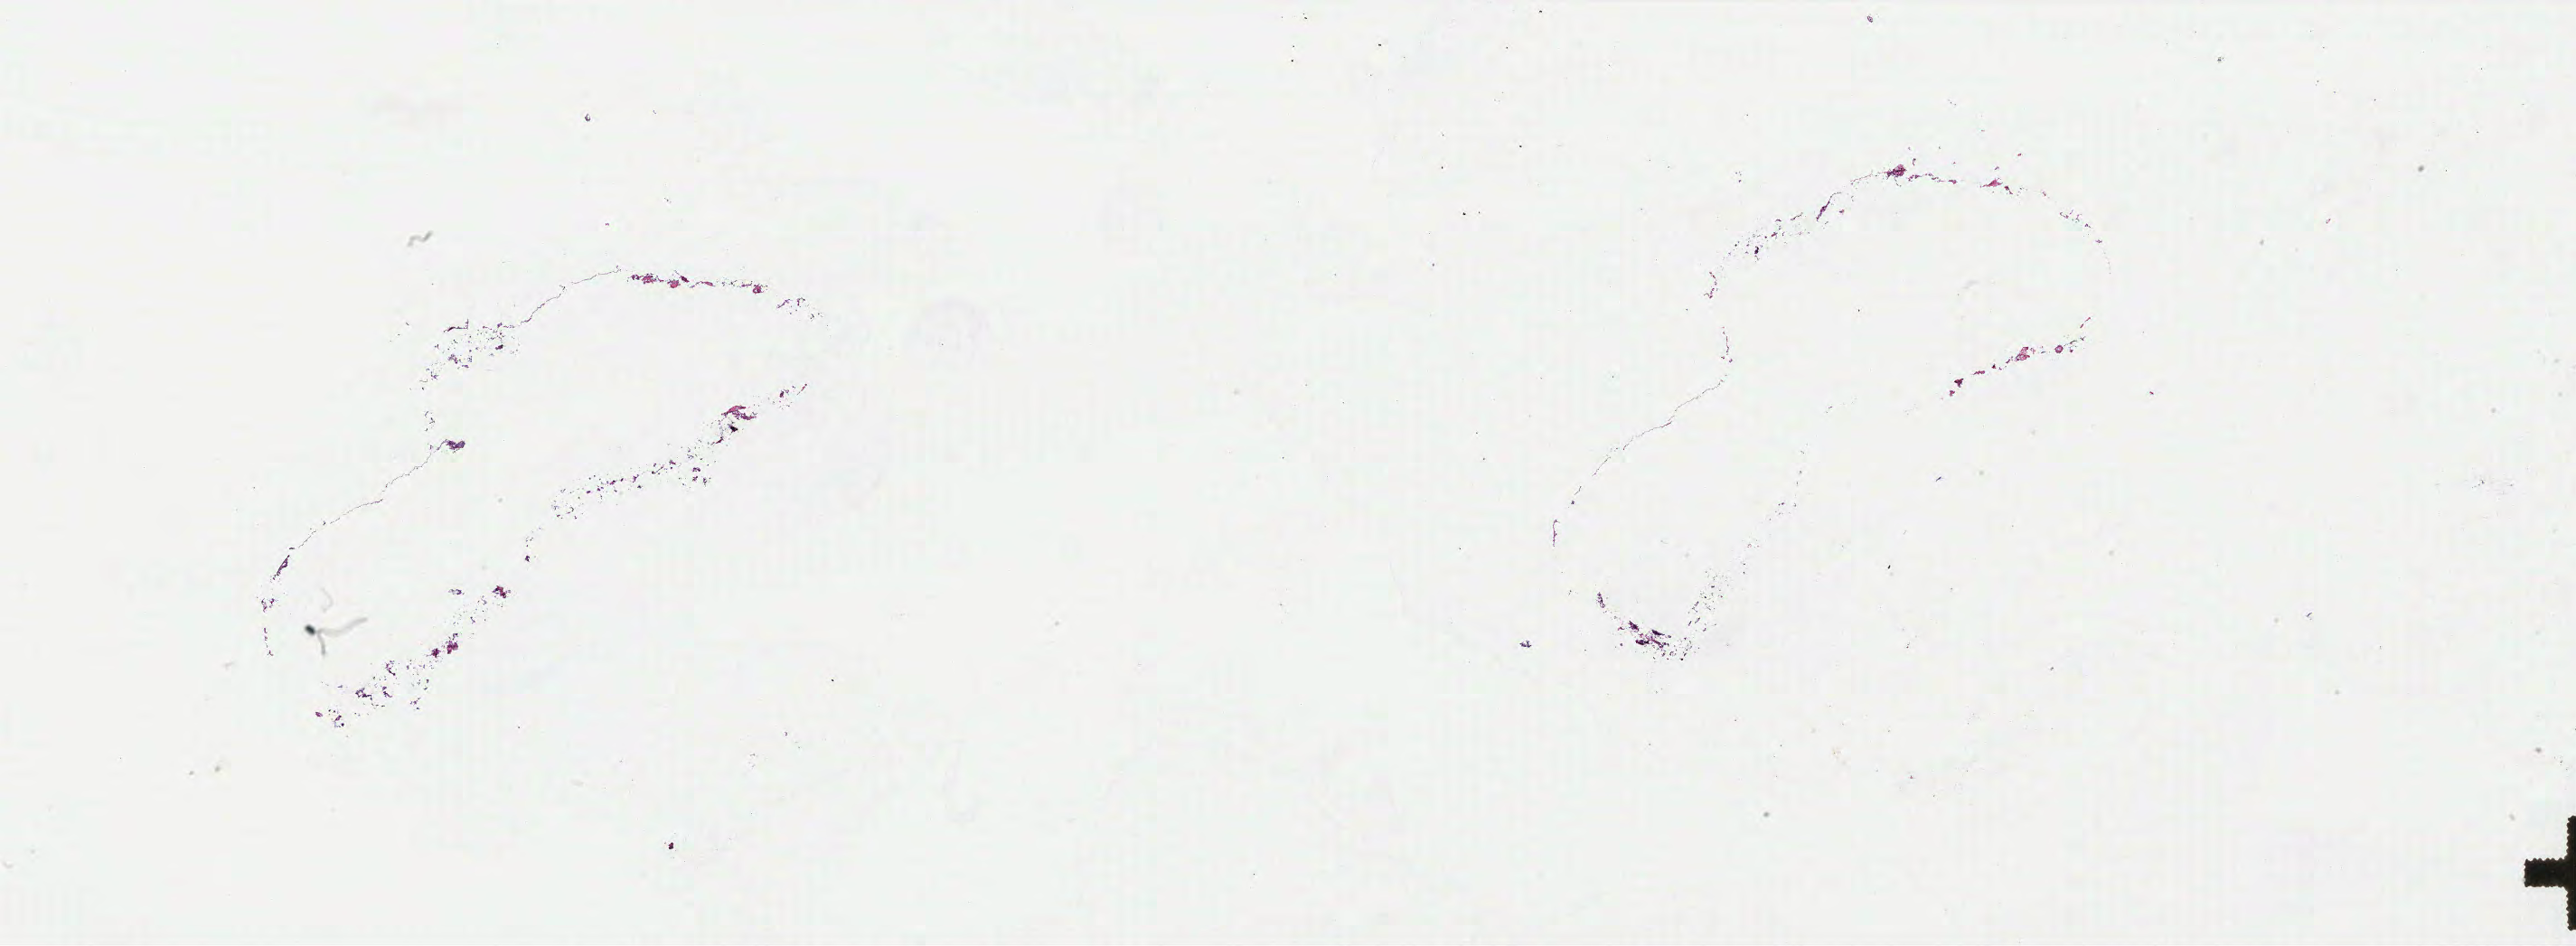
Whole-slide histology image, H&E-stained, shown as a low-resolution overview of the whole scanned area (about 45.6 x 16.8 mm, acquisition: 40x scan). Ovary, tissue type not recorded.
Patient diagnosis (cohort enrolment): ovarian cancer (ovary).